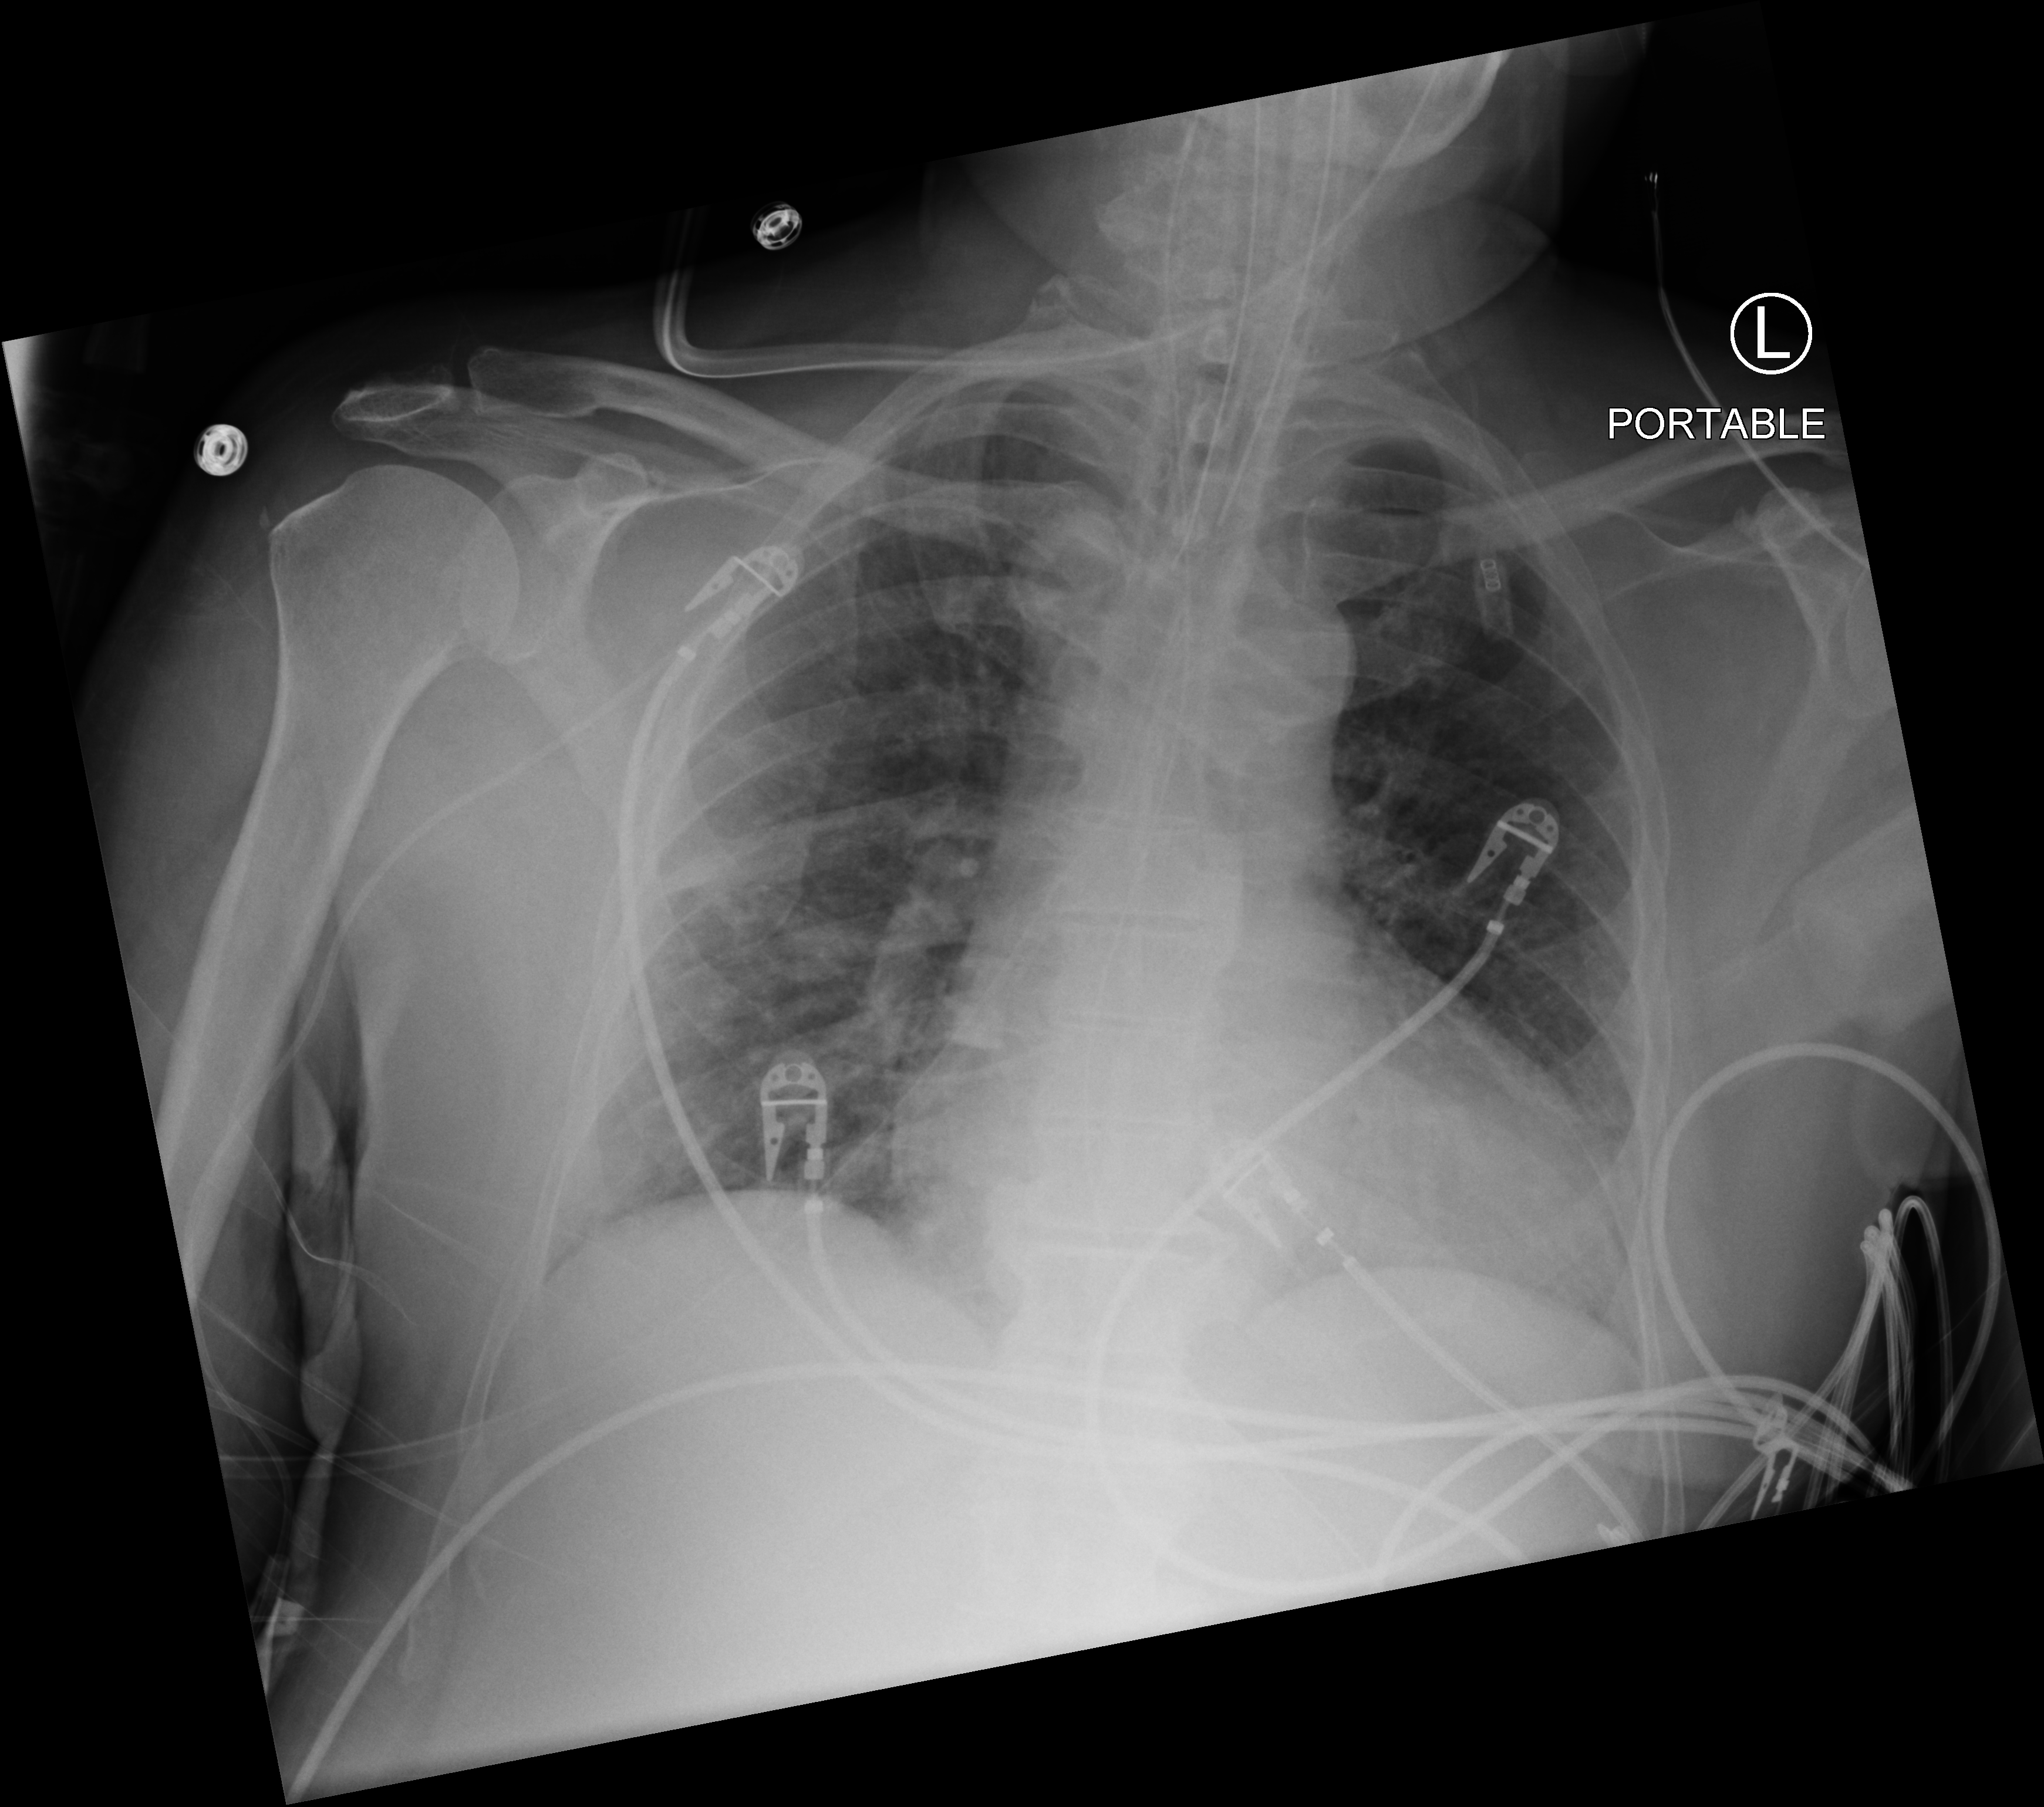
Bedside chest radiograph (computed radiography); anteroposterior (AP) projection. Patient hospitalised with COVID-19; male, aged 60–74 years.
Admission-level facts for this patient (not findings on this image; timing relative to this image not recorded):
- admitted to intensive care during this hospital stay: yes